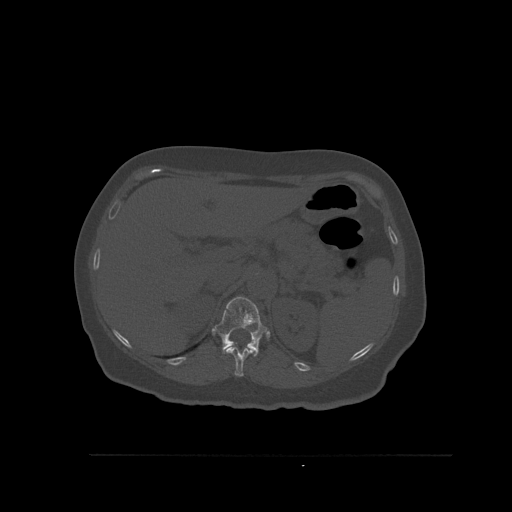
CT including the spine, one axial slice. Slice 292 of 527 in the series (ordered by position). Bone window (W 1800 / L 400 HU). 1.5 mm slice thickness. 512 × 512 image matrix, field of view 470 × 470 mm. Patient: female, 73 years. From the clinical record (not read from this slice): primary cancer: breast.
Annotated regions visible in this slice (semi-automatic segmentation, software-assisted and operator-edited):
- T11 vertebra: bounding box <222,346,255,377> (left, top, right, bottom; pixels)
- T12 vertebra: <214,296,268,357>